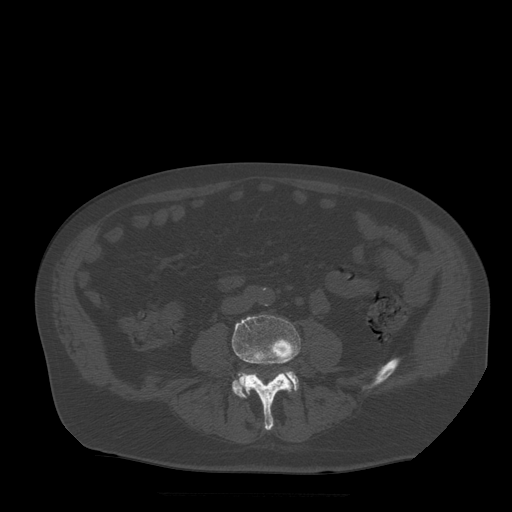
CT including the spine, one axial slice; position 110 of 522 along the scan axis; bone window (W 1800 / L 400 HU); 1.25 mm slice thickness; 512 × 512 image matrix, field of view 420 × 420 mm. Patient age 72 years. Case-level facts recorded for this patient, not image findings: primary cancer: prostate.
Annotated regions visible in this slice (semi-automatic segmentation, software-assisted and operator-edited):
- L4 vertebra: bounding box (x1, y1, x2, y2) in pixels: (232, 315, 301, 431)
- L5 vertebra: (232, 371, 299, 398)